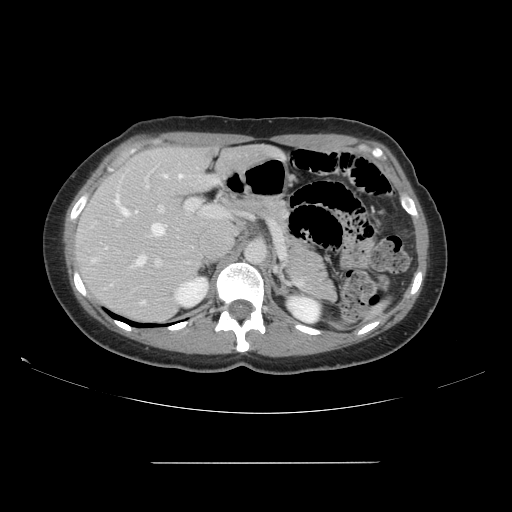
Contrast-enhanced abdominal CT, one axial slice. 120 kVp. Soft-tissue window (W 400 / L 40 HU). 2.5 mm slice thickness. 512 × 512 image matrix, field of view 421 × 421 mm. Female patient, age 46 years. Case-level facts recorded for this patient, not image findings: diagnosis: colorectal cancer liver metastases, imaged before liver resection; multiple liver metastases: yes; largest metastasis: 3 cm; disease in both lobes: yes.
Annotated regions visible in this slice (outlined manually by an expert reader):
- hepatic veins: box from (x=114, y=174) to (x=183, y=267) px
- liver: (x=75, y=148)–(x=270, y=323)
- planned liver remnant (the part of the liver to remain after resection): (x=89, y=149)–(x=216, y=256)
- portal vein (with intrahepatic branches): (x=117, y=170)–(x=223, y=303)